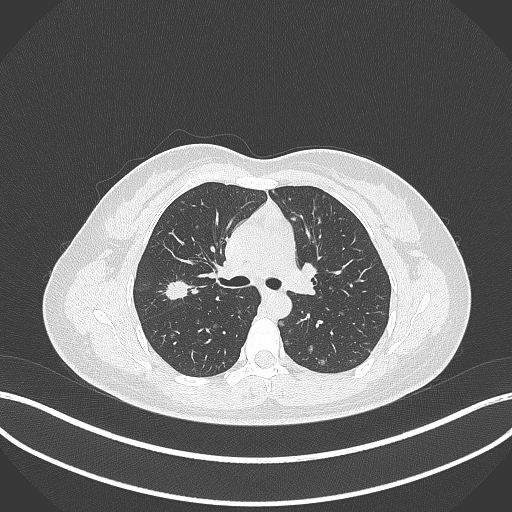
Chest CT, one axial slice. Position 213 of 307 along the scan axis. 120 kVp. Lung window (W 1500 / L -600 HU). 1 mm slice thickness. 512 × 512 image matrix, field of view 400 × 400 mm. Female patient, age 33 years. Case-level facts recorded for this patient, not image findings: clinical TNM (as recorded): T1c N0 M0; histopathological grade: G2-G3.
Structures marked on this image (rectangle marked by the reading radiologist):
- lung tumour (recorded histology: adenocarcinoma): bounding box <162,278,191,303> (left, top, right, bottom; pixels)